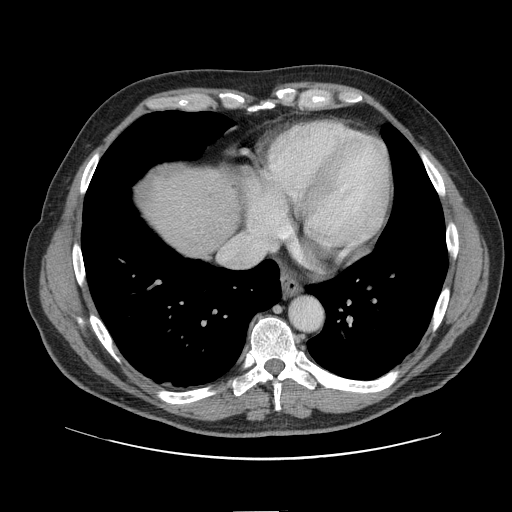
Contrast-enhanced abdominal CT, one axial slice; slice 140 of 161 in the series (ordered by position); intravenous contrast given; soft-tissue window (W 400 / L 40 HU); 512 × 512 image matrix, field of view 412 × 412 mm. Male patient, age 66 years. Case-level facts recorded for this patient, not image findings: diagnosis: colorectal cancer liver metastases, imaged before liver resection; multiple liver metastases: no; largest metastasis: 3.5 cm.
Structures marked on this image (outlined manually by an expert reader):
- hepatic veins: bounding box <220,237,241,261> (left, top, right, bottom; pixels)
- liver: <144,169,239,256>
- planned liver remnant (the part of the liver to remain after resection): <144,171,239,257>
- liver metastasis: <210,195,215,200>